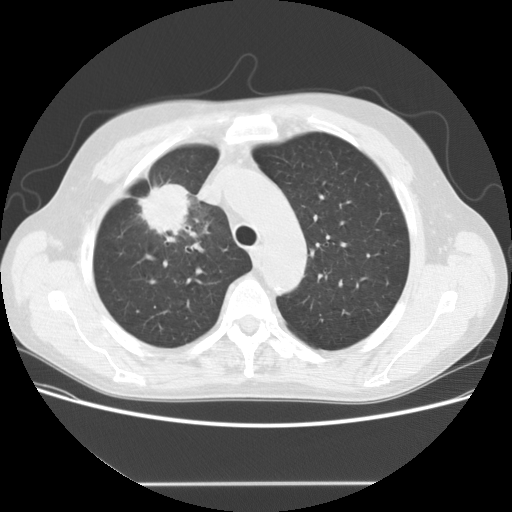
Low-dose screening chest CT, one axial slice. Position 117 of 153 along the scan axis. 120 kVp. Lung window (W 1500 / L -600 HU). 2.5 mm slice thickness. 512 × 512 image matrix.
Outlined on this slice (outlined manually by an expert reader):
- lesion 1 (tumor, upper lobe of right lung): bounding box (x1, y1, x2, y2) in pixels: (138, 182, 192, 243)